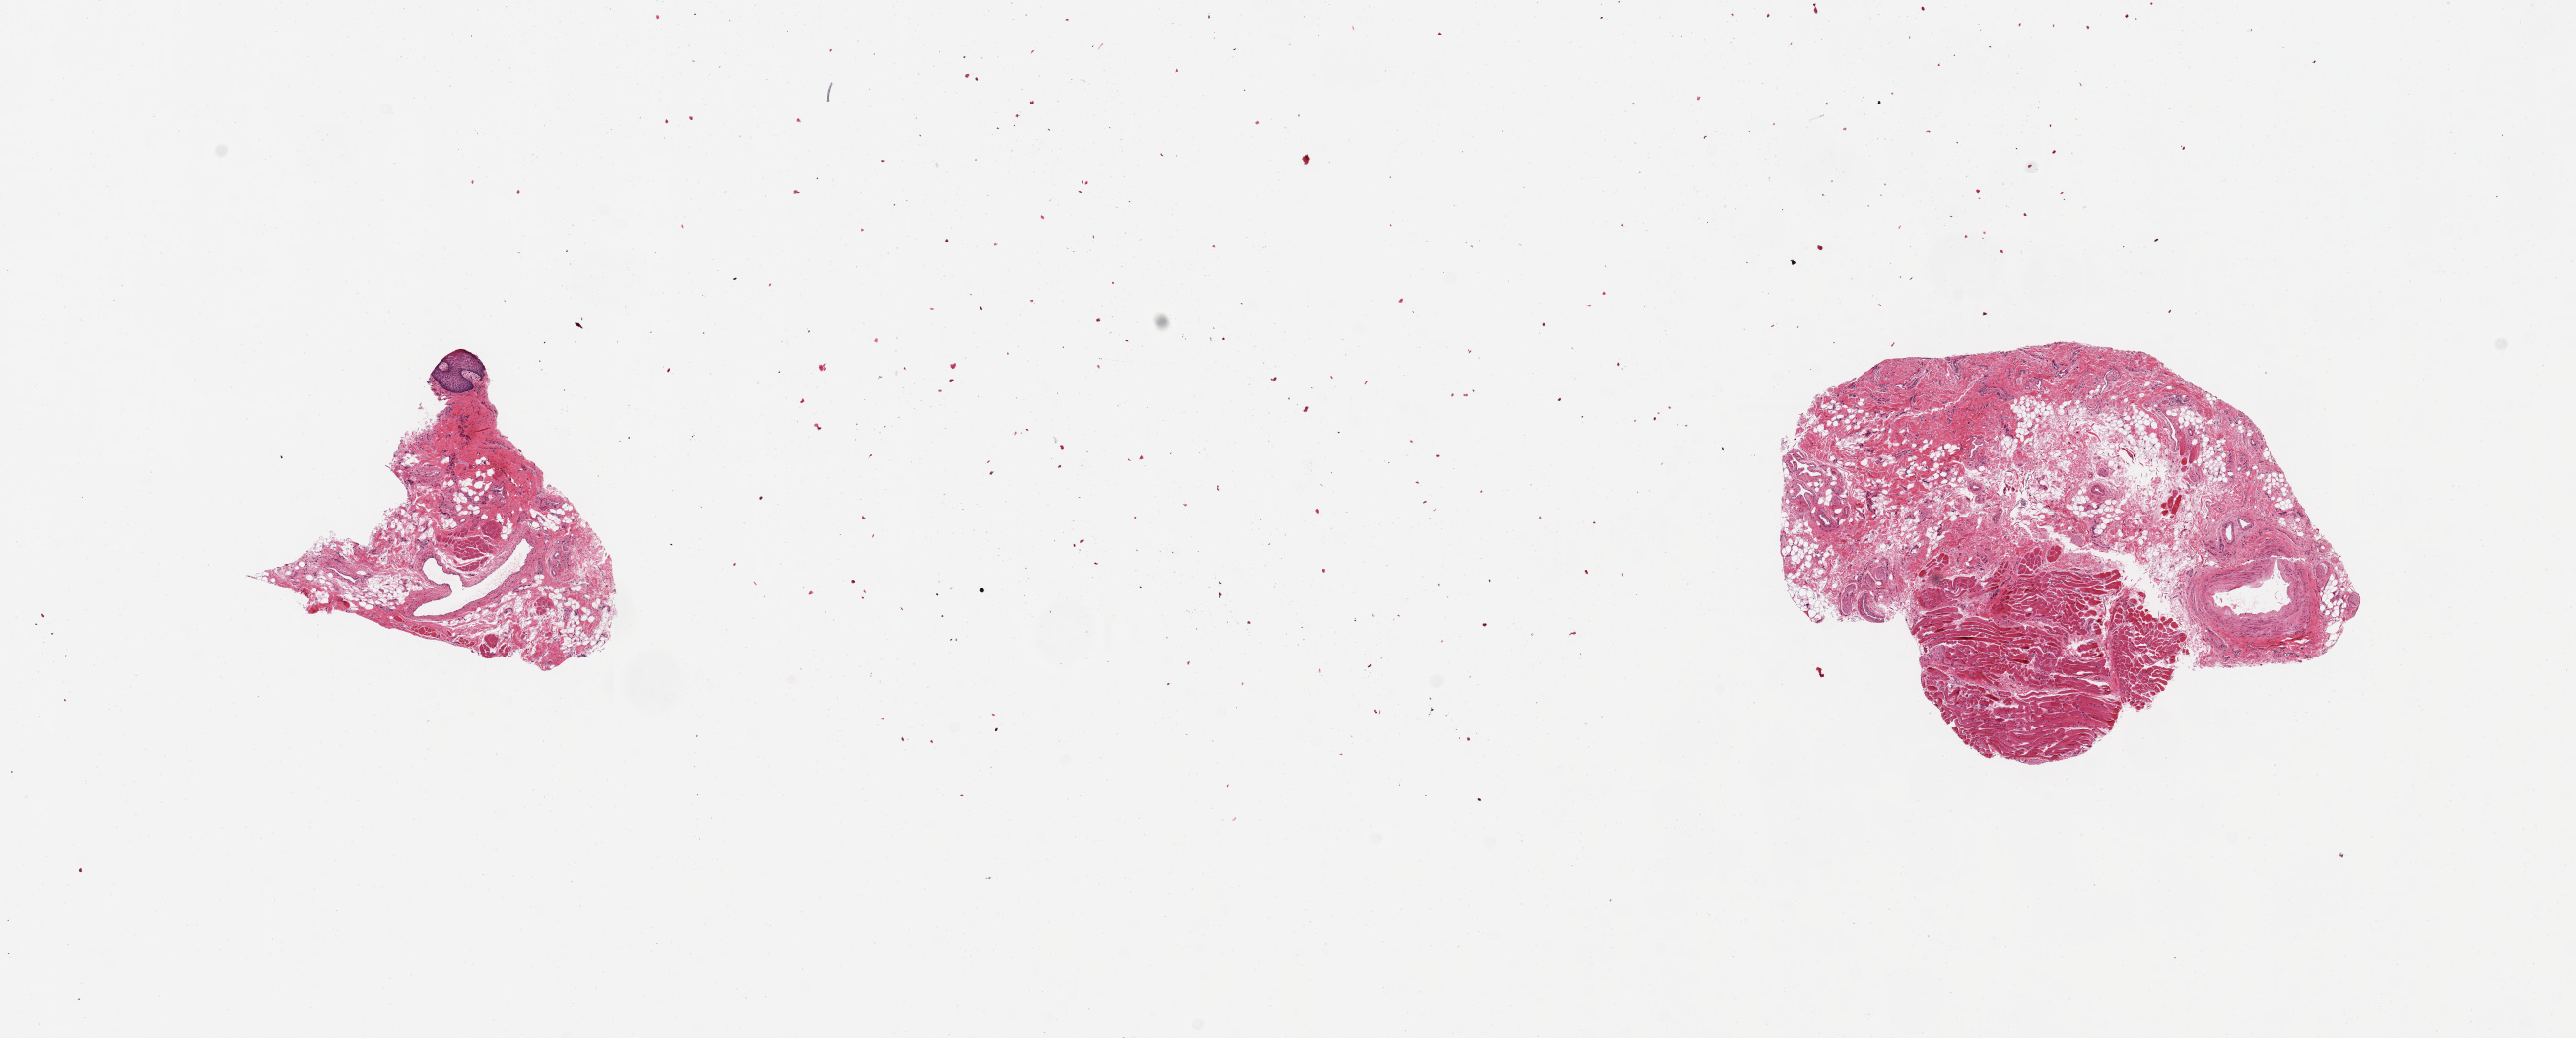
Digitized hematoxylin and eosin (H&E)-stained section — a low-resolution overview of the entire scanned area, about 20.7 x 8.3 mm (acquisition: 20x scan). PAXgene-fixed paraffin-embedded (PFPE) section. Target tissue: minor salivary gland. Donor tissue sample. Male donor.
* review note (as recorded): 2 pieces; no salivary gland tissue; skin, muscle, fat , blood vessels, stroma